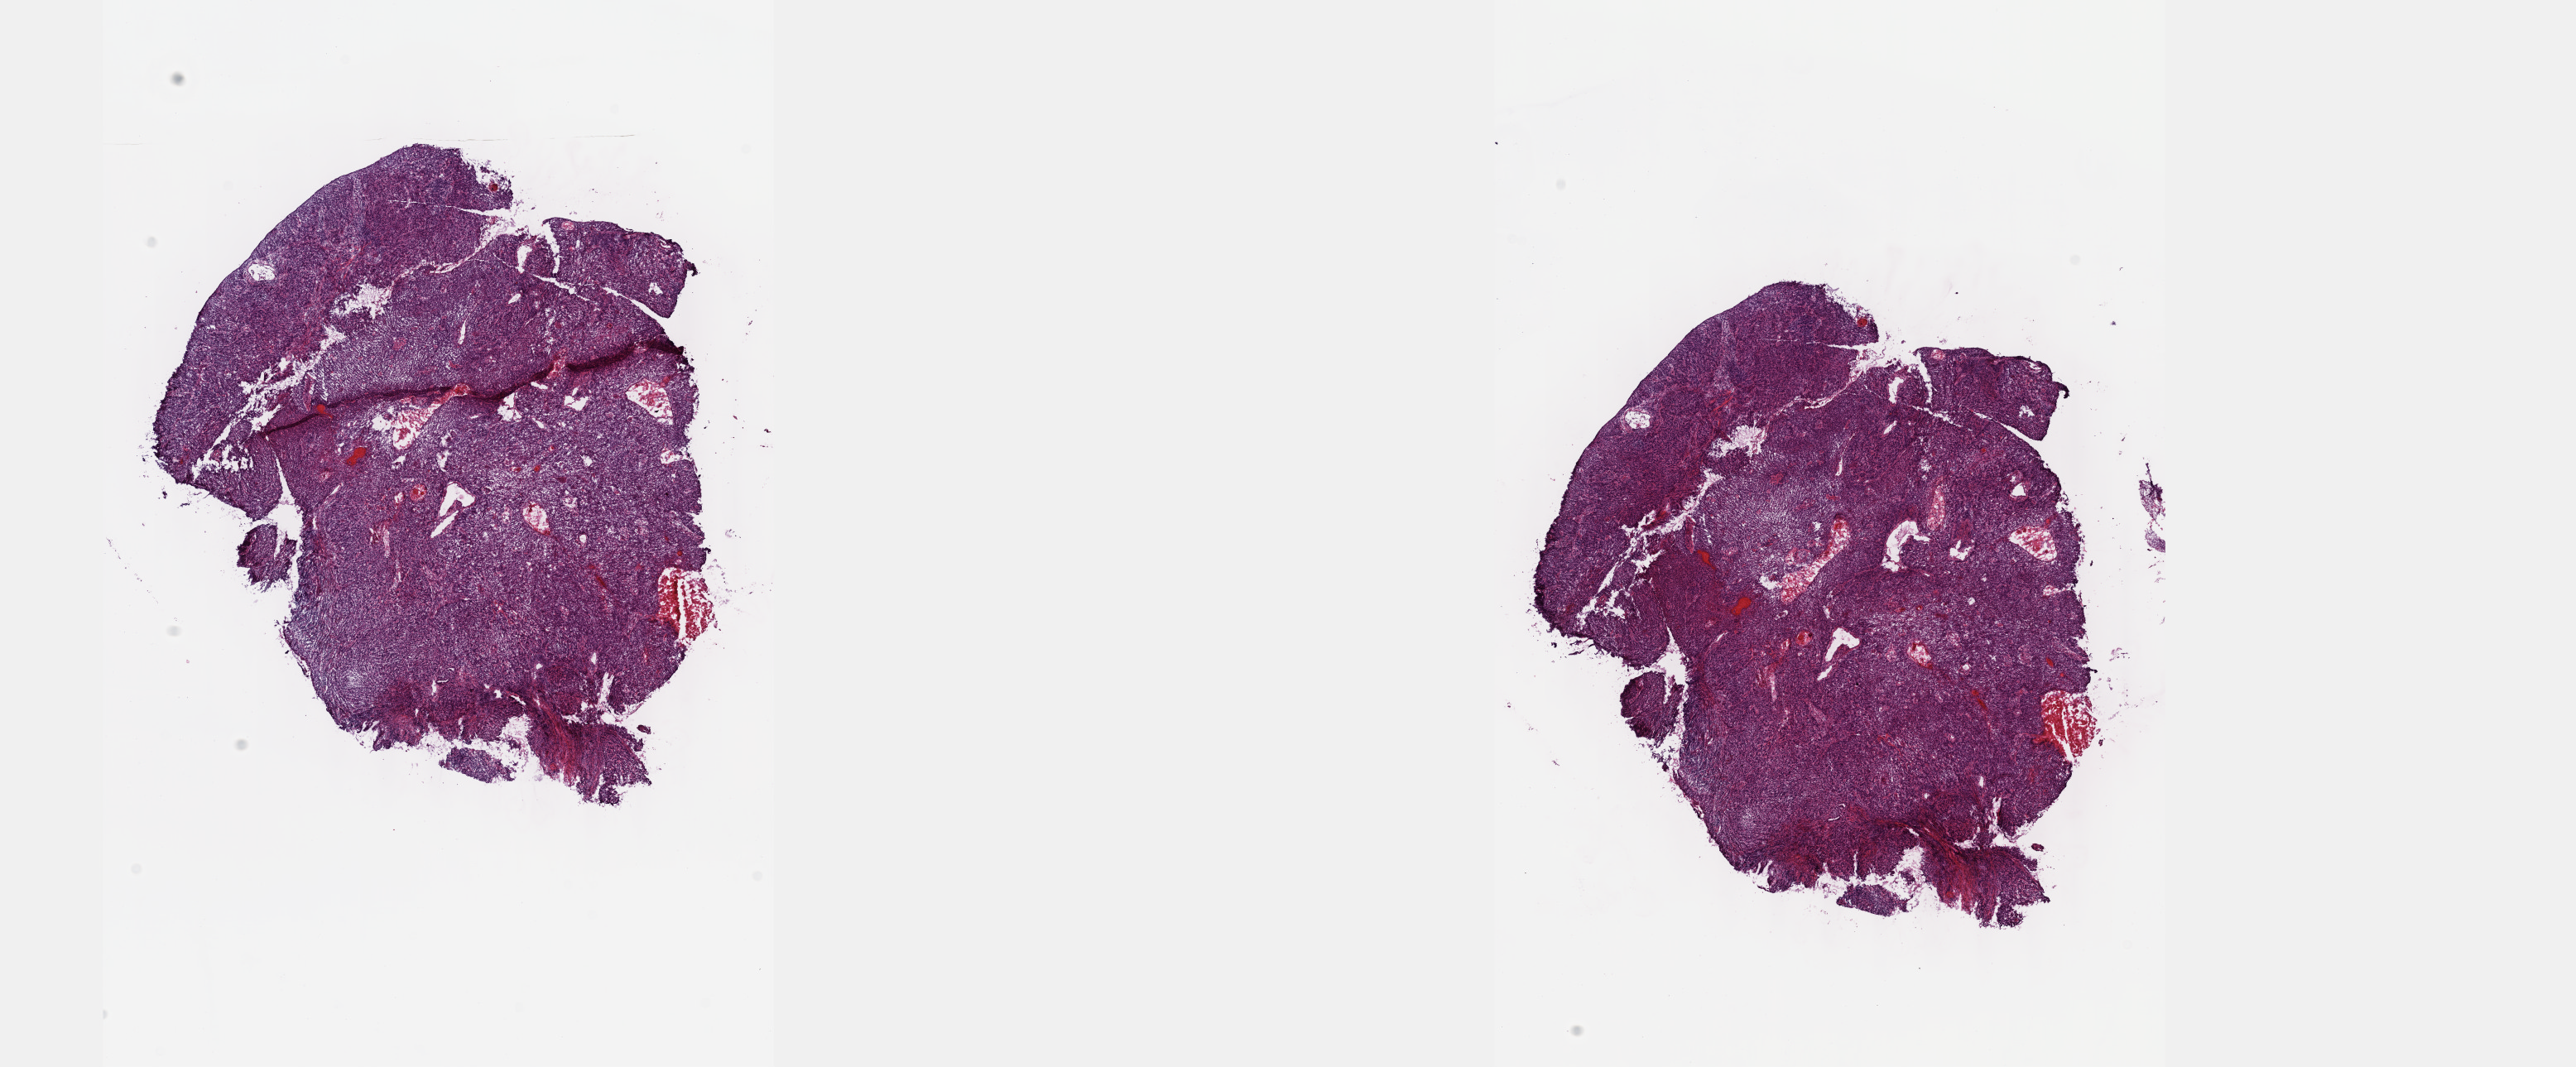
H&E-stained whole-slide image — shown as a low-resolution overview of the whole scanned area (about 25.1 x 10.4 mm); frozen section from the top of the tissue portion; cervix, primary tumour sample. Female, age 39 years at initial diagnosis.
Diagnosis: Squamous cell carcinoma, NOS (cervix uteri).